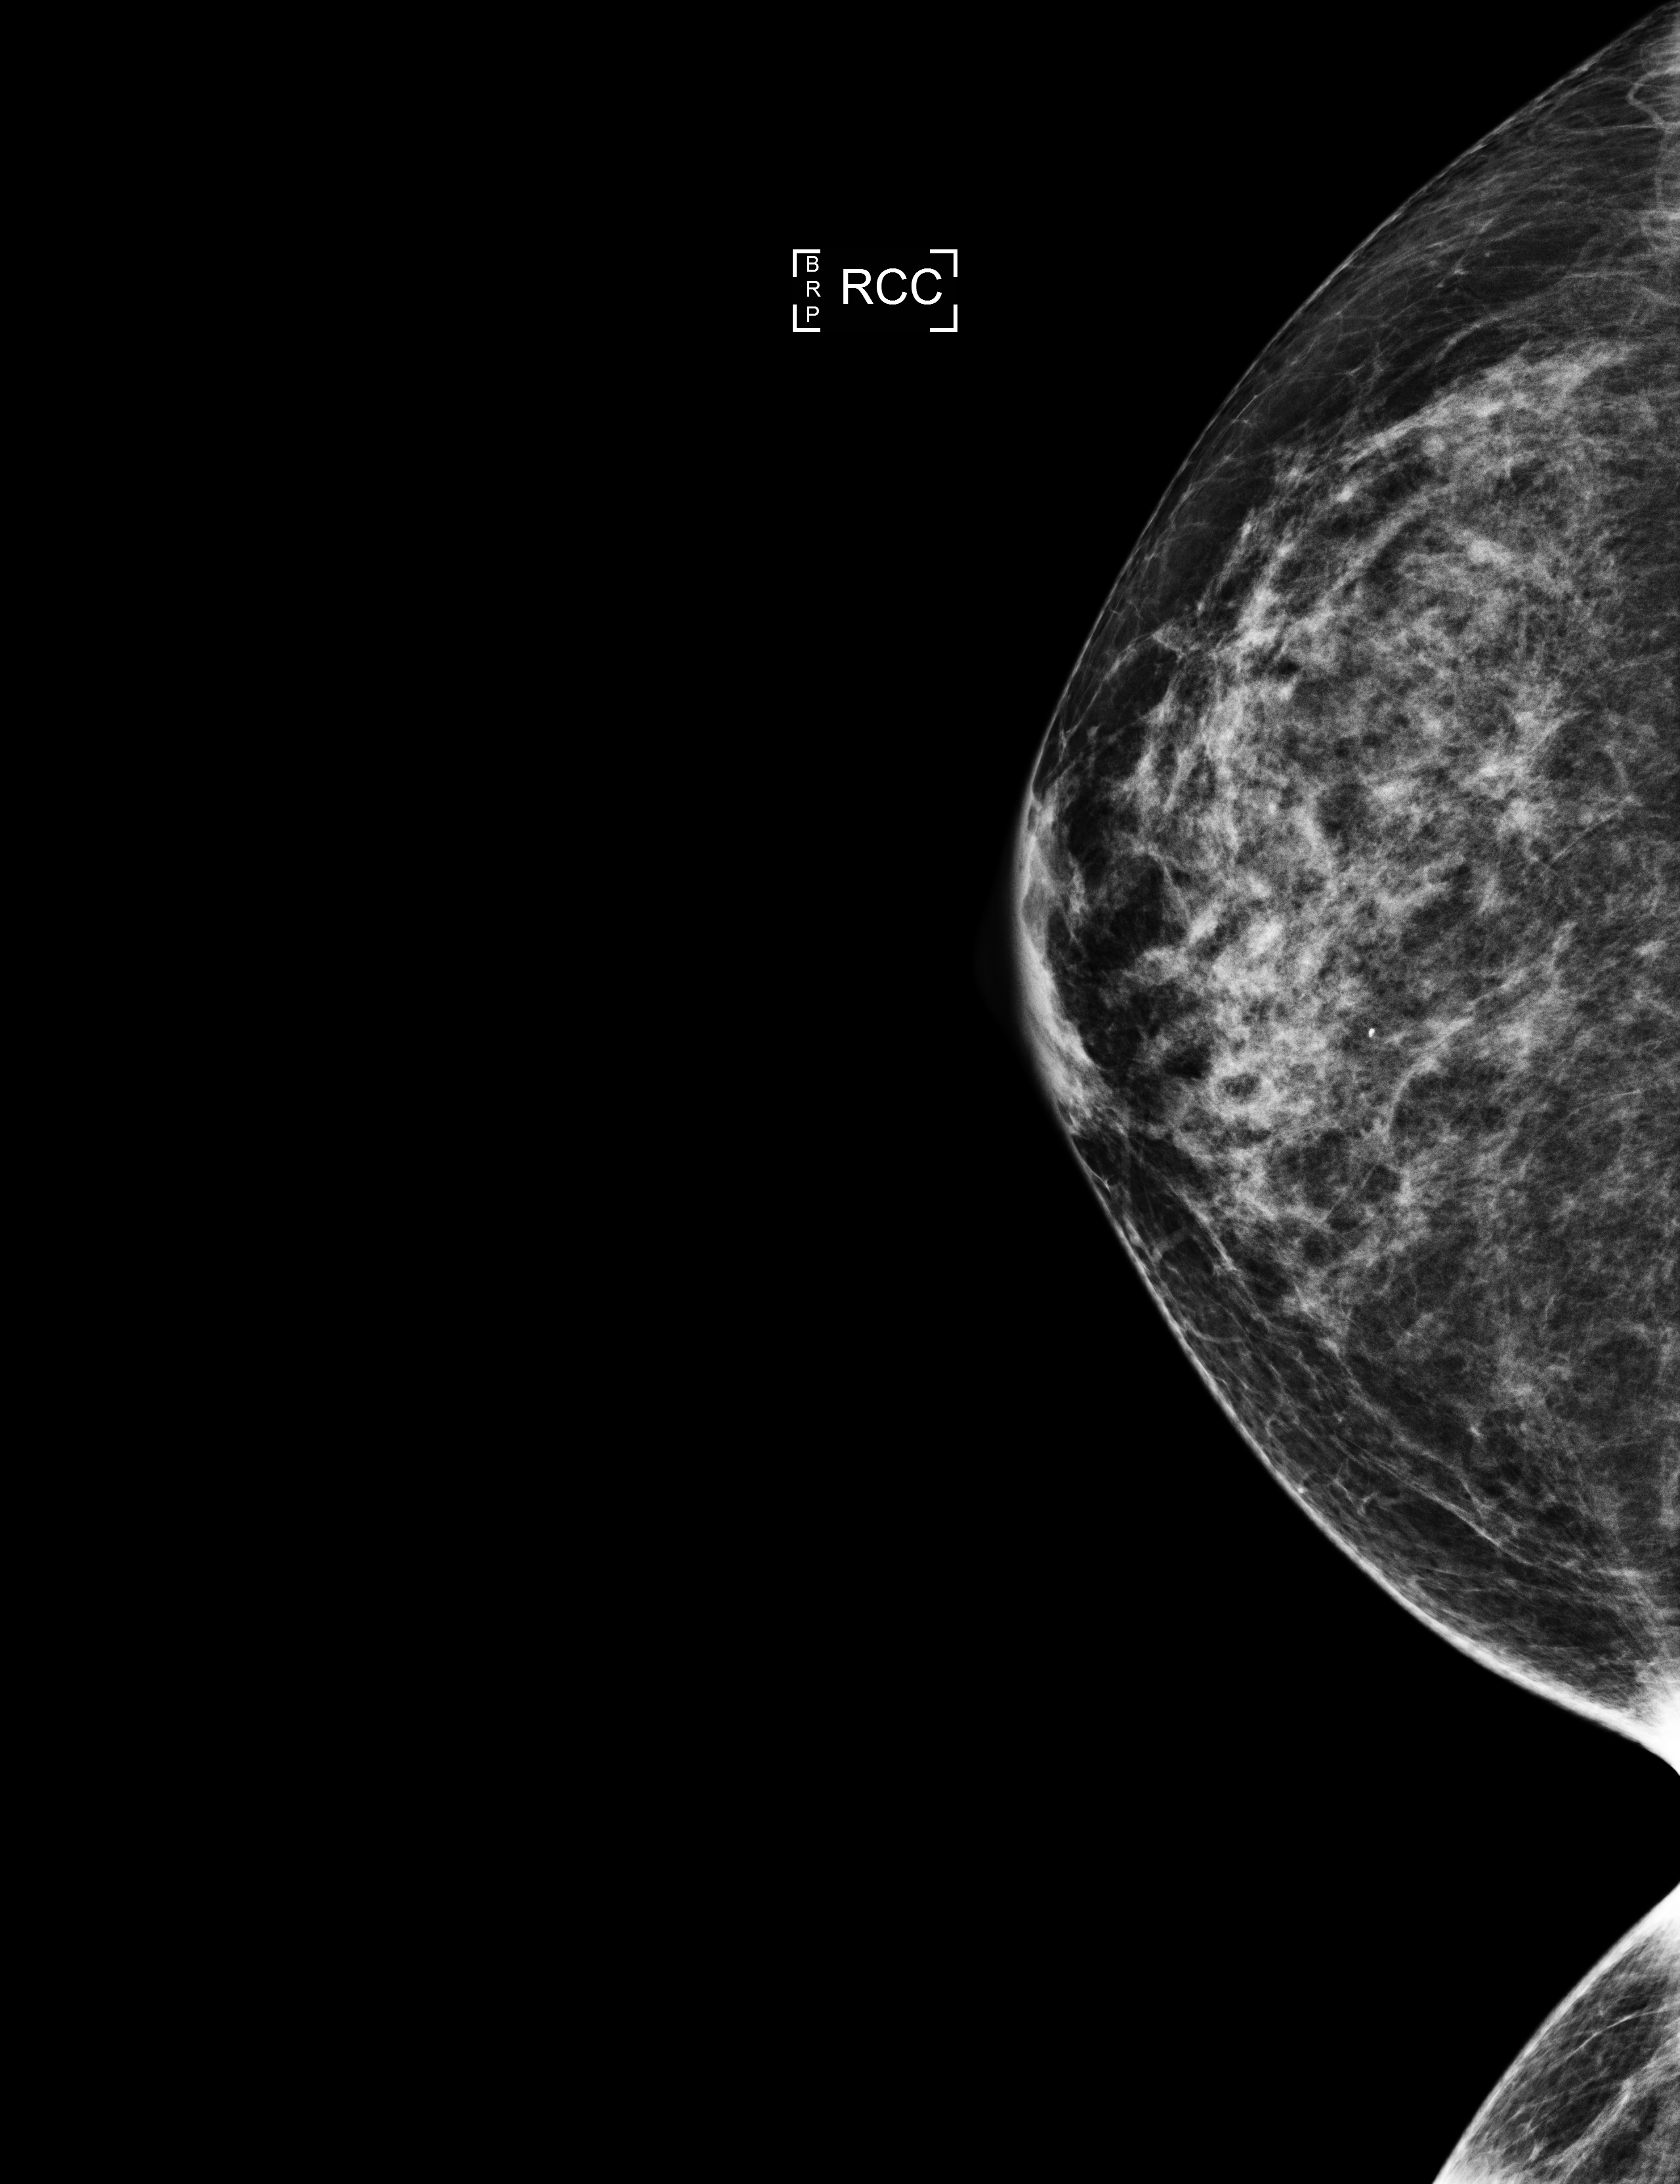
Annual screening mammography examination. Female patient, age 63 years.
Image type: full-field digital mammogram. Breast: right. Projection: craniocaudal (CC) view.